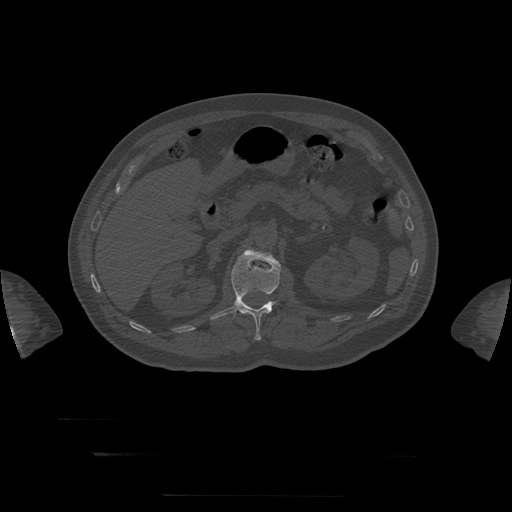
CT including the spine, one axial slice. Slice 46 of 397 in the series (ordered by position). 120 kVp. Bone window (W 1800 / L 400 HU). 1.25 mm slice thickness. 512 × 512 image matrix, field of view 510 × 510 mm. Patient age 73 years. From the clinical record (not read from this slice): primary cancer: prostate.
Structures marked on this image (semi-automatic segmentation, software-assisted and operator-edited):
- L1 vertebra: bounding box <210,250,281,341> (left, top, right, bottom; pixels)